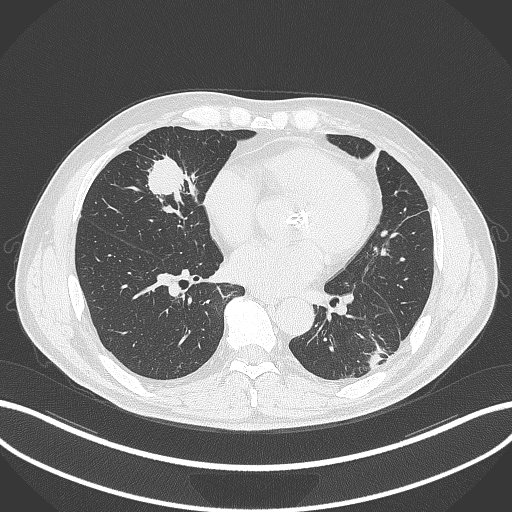
Chest CT, one axial slice. Position 119 of 399 along the scan axis. Reconstruction kernel B70f. Lung window (W 1500 / L -600 HU). 1 mm slice thickness. 512 × 512 image matrix, field of view 400 × 400 mm. Patient: male, 59 years. Case-level facts recorded for this patient, not image findings: clinical TNM (as recorded): T2a N1 M0.
Structures marked on this image (rectangle marked by the reading radiologist):
- lung tumour (recorded histology: adenocarcinoma): bounding box <141,150,193,212> (left, top, right, bottom; pixels)